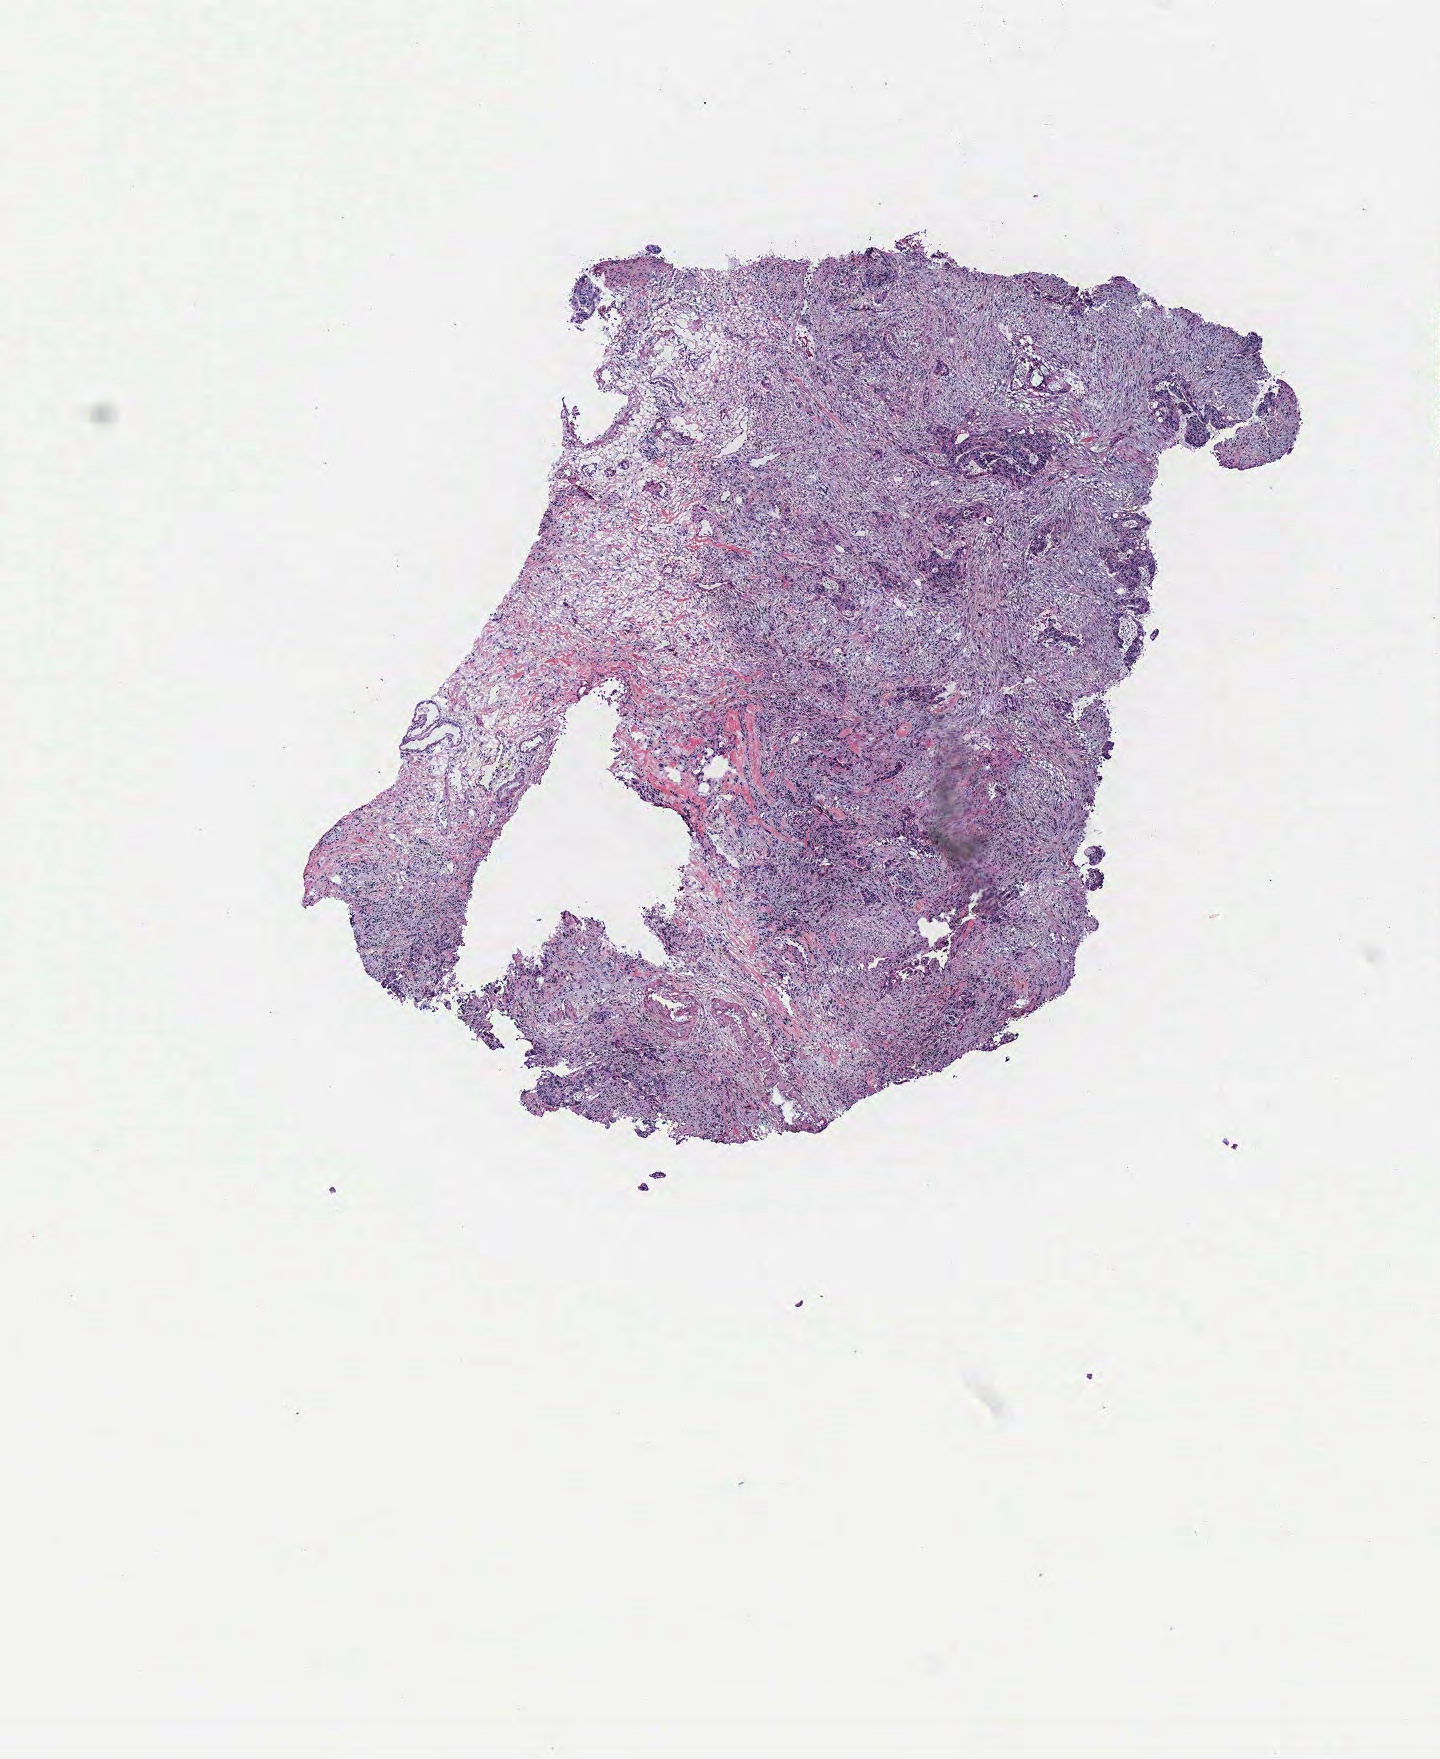
H&E whole-slide image, shown as a low-resolution overview of the whole scanned area (about 5.8 x 7.0 mm); colon, tissue type not recorded.
Patient diagnosis (cohort enrolment): colon cancer (colon).